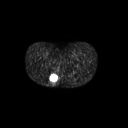
FDG PET of an extremity soft-tissue mass (from a PET/CT study), one axial slice. Position 19 of 267 along the scan axis. 128 × 128 image matrix, field of view 700 × 700 mm. Patient: female, 17 years. Case-level facts recorded for this patient, not image findings: histological type: epithelioid sarcoma; grade: intermediate; site of the primary tumour: right buttock.
Annotated regions visible in this slice (expert contour drawn on MRI and transferred to this co-registered scan by the dataset authors):
- gross tumour volume including surrounding oedema: bounding box [x1, y1, x2, y2] px = [49, 73, 60, 87]
- gross tumour volume (mass): [50, 74, 58, 81]